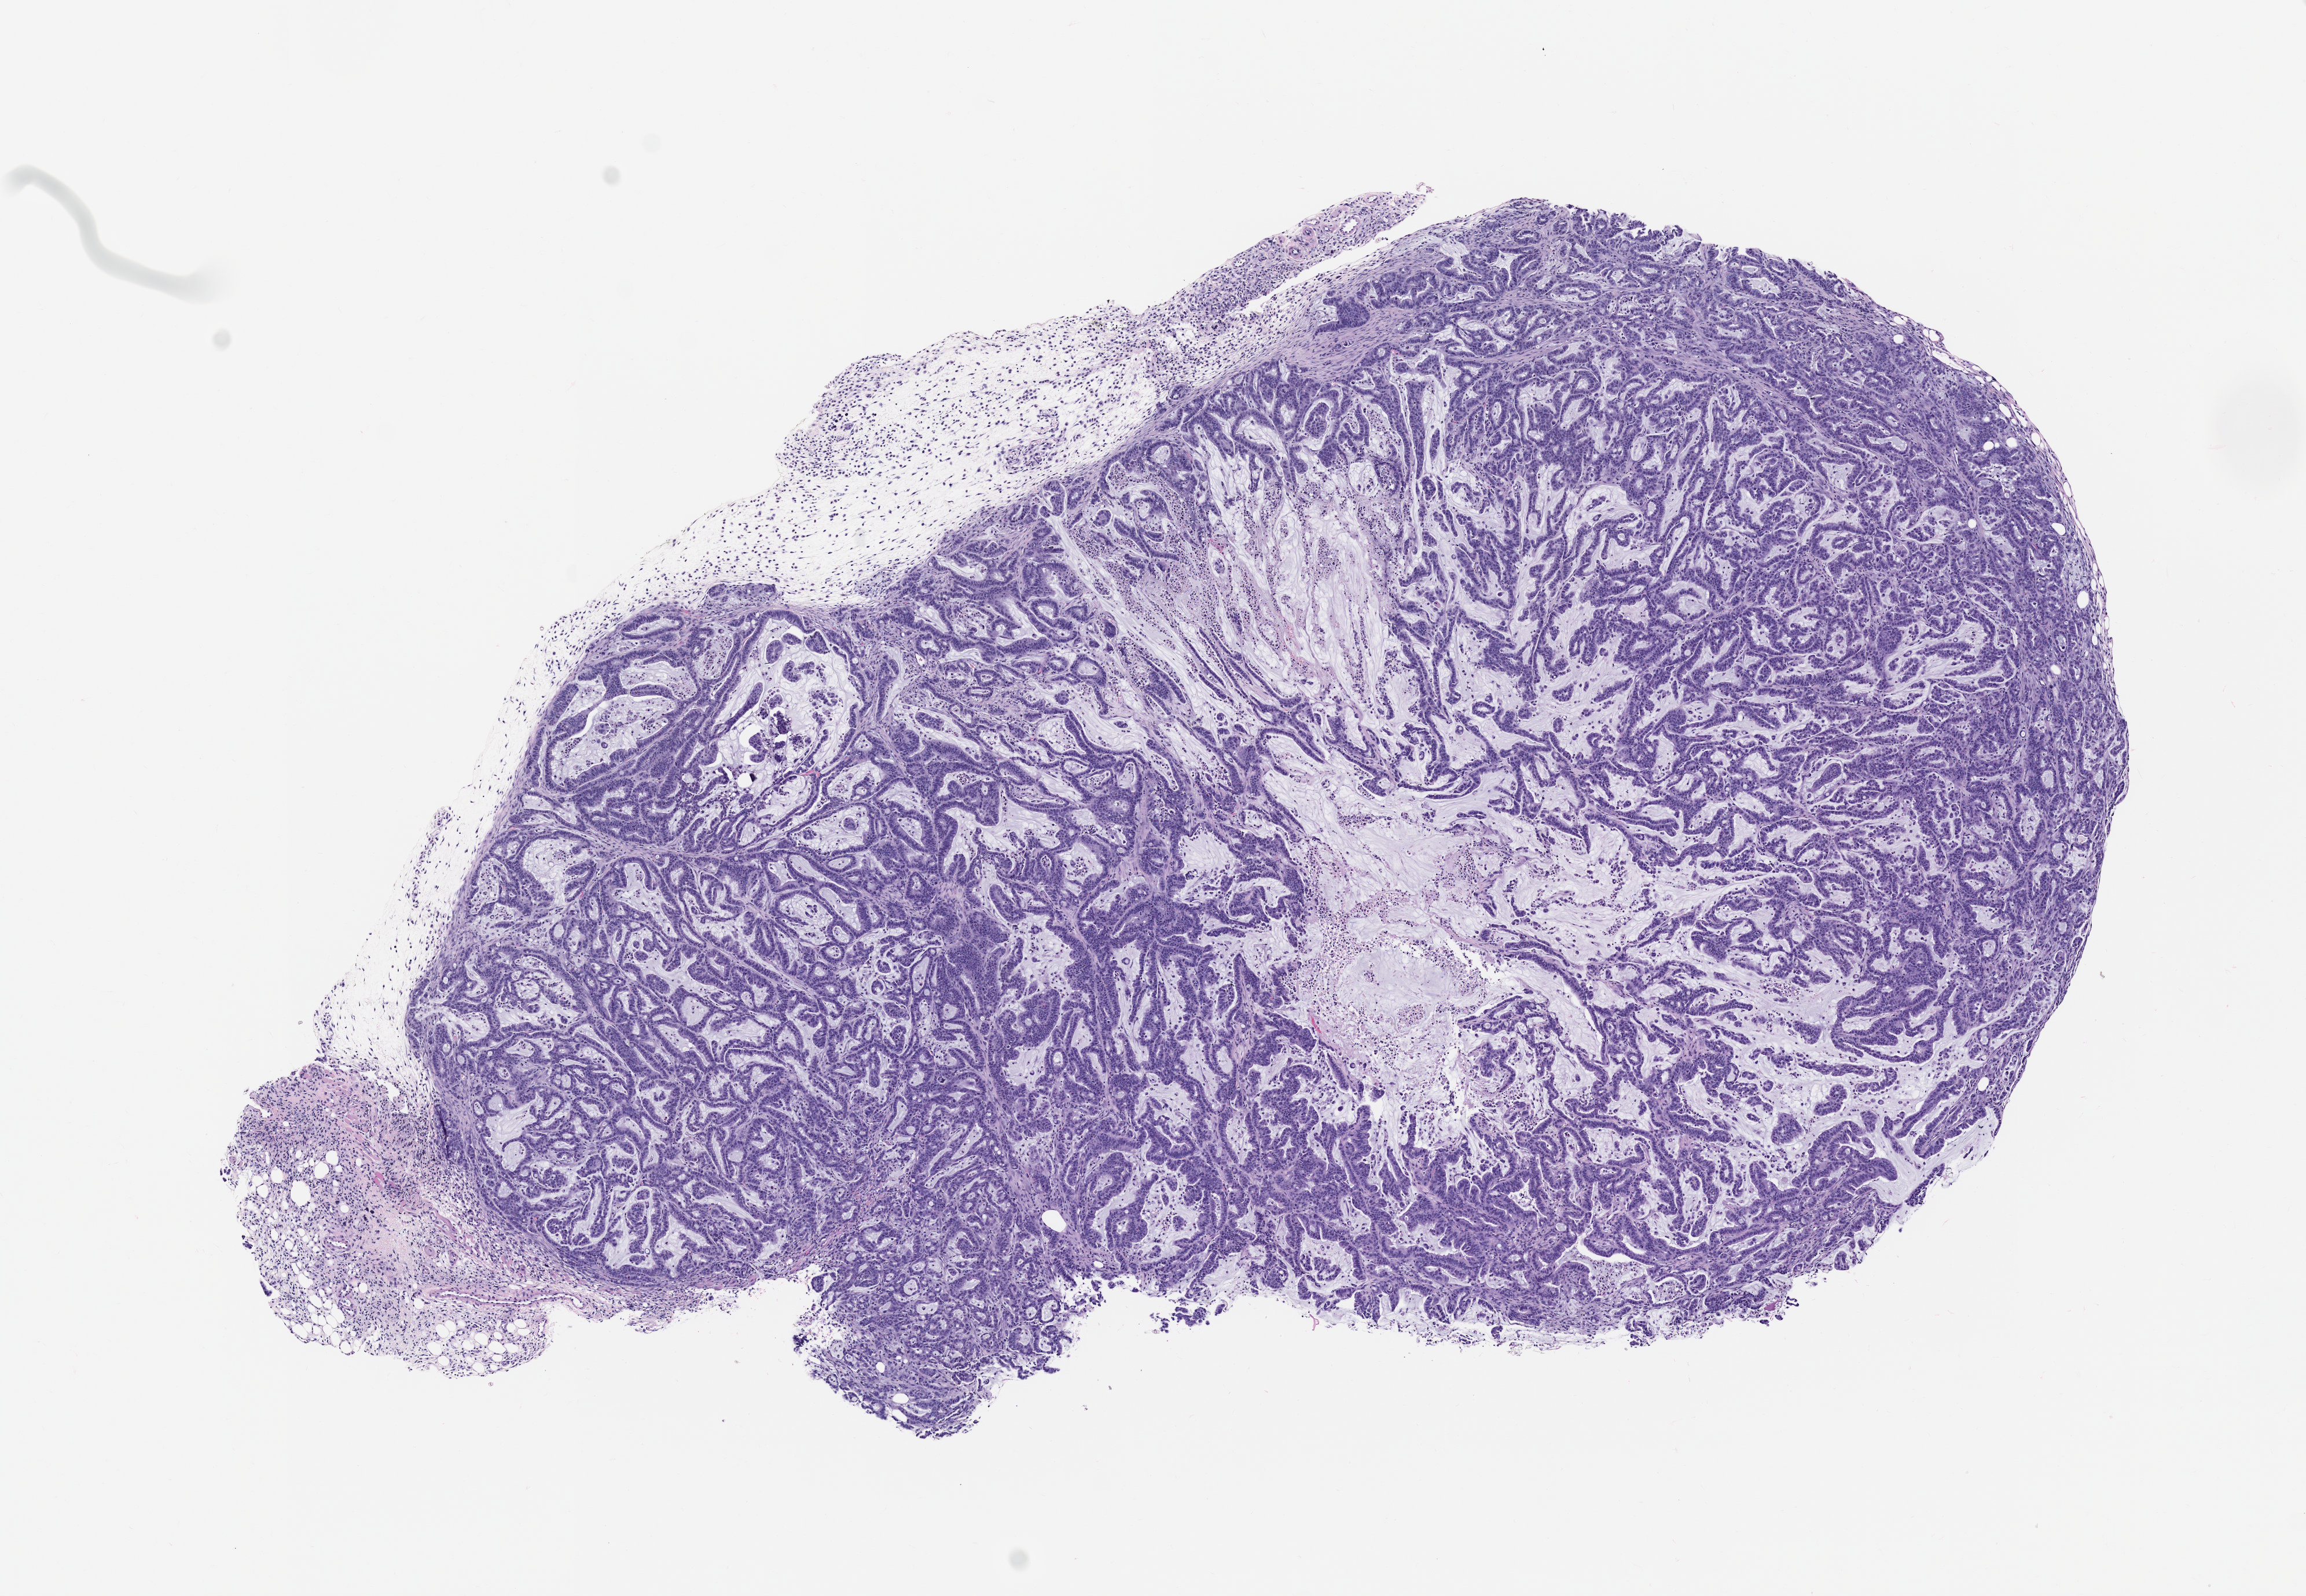
Whole-slide image, haematoxylin and eosin: patient-derived xenograft (human tumor grown in a mouse), passage 1 — low-resolution overview of the scanned area, about 8.0 x 5.5 mm, FFPE section, originating tumor site category: colon.
Originating patient diagnosis: Colon Adenocarcinoma.